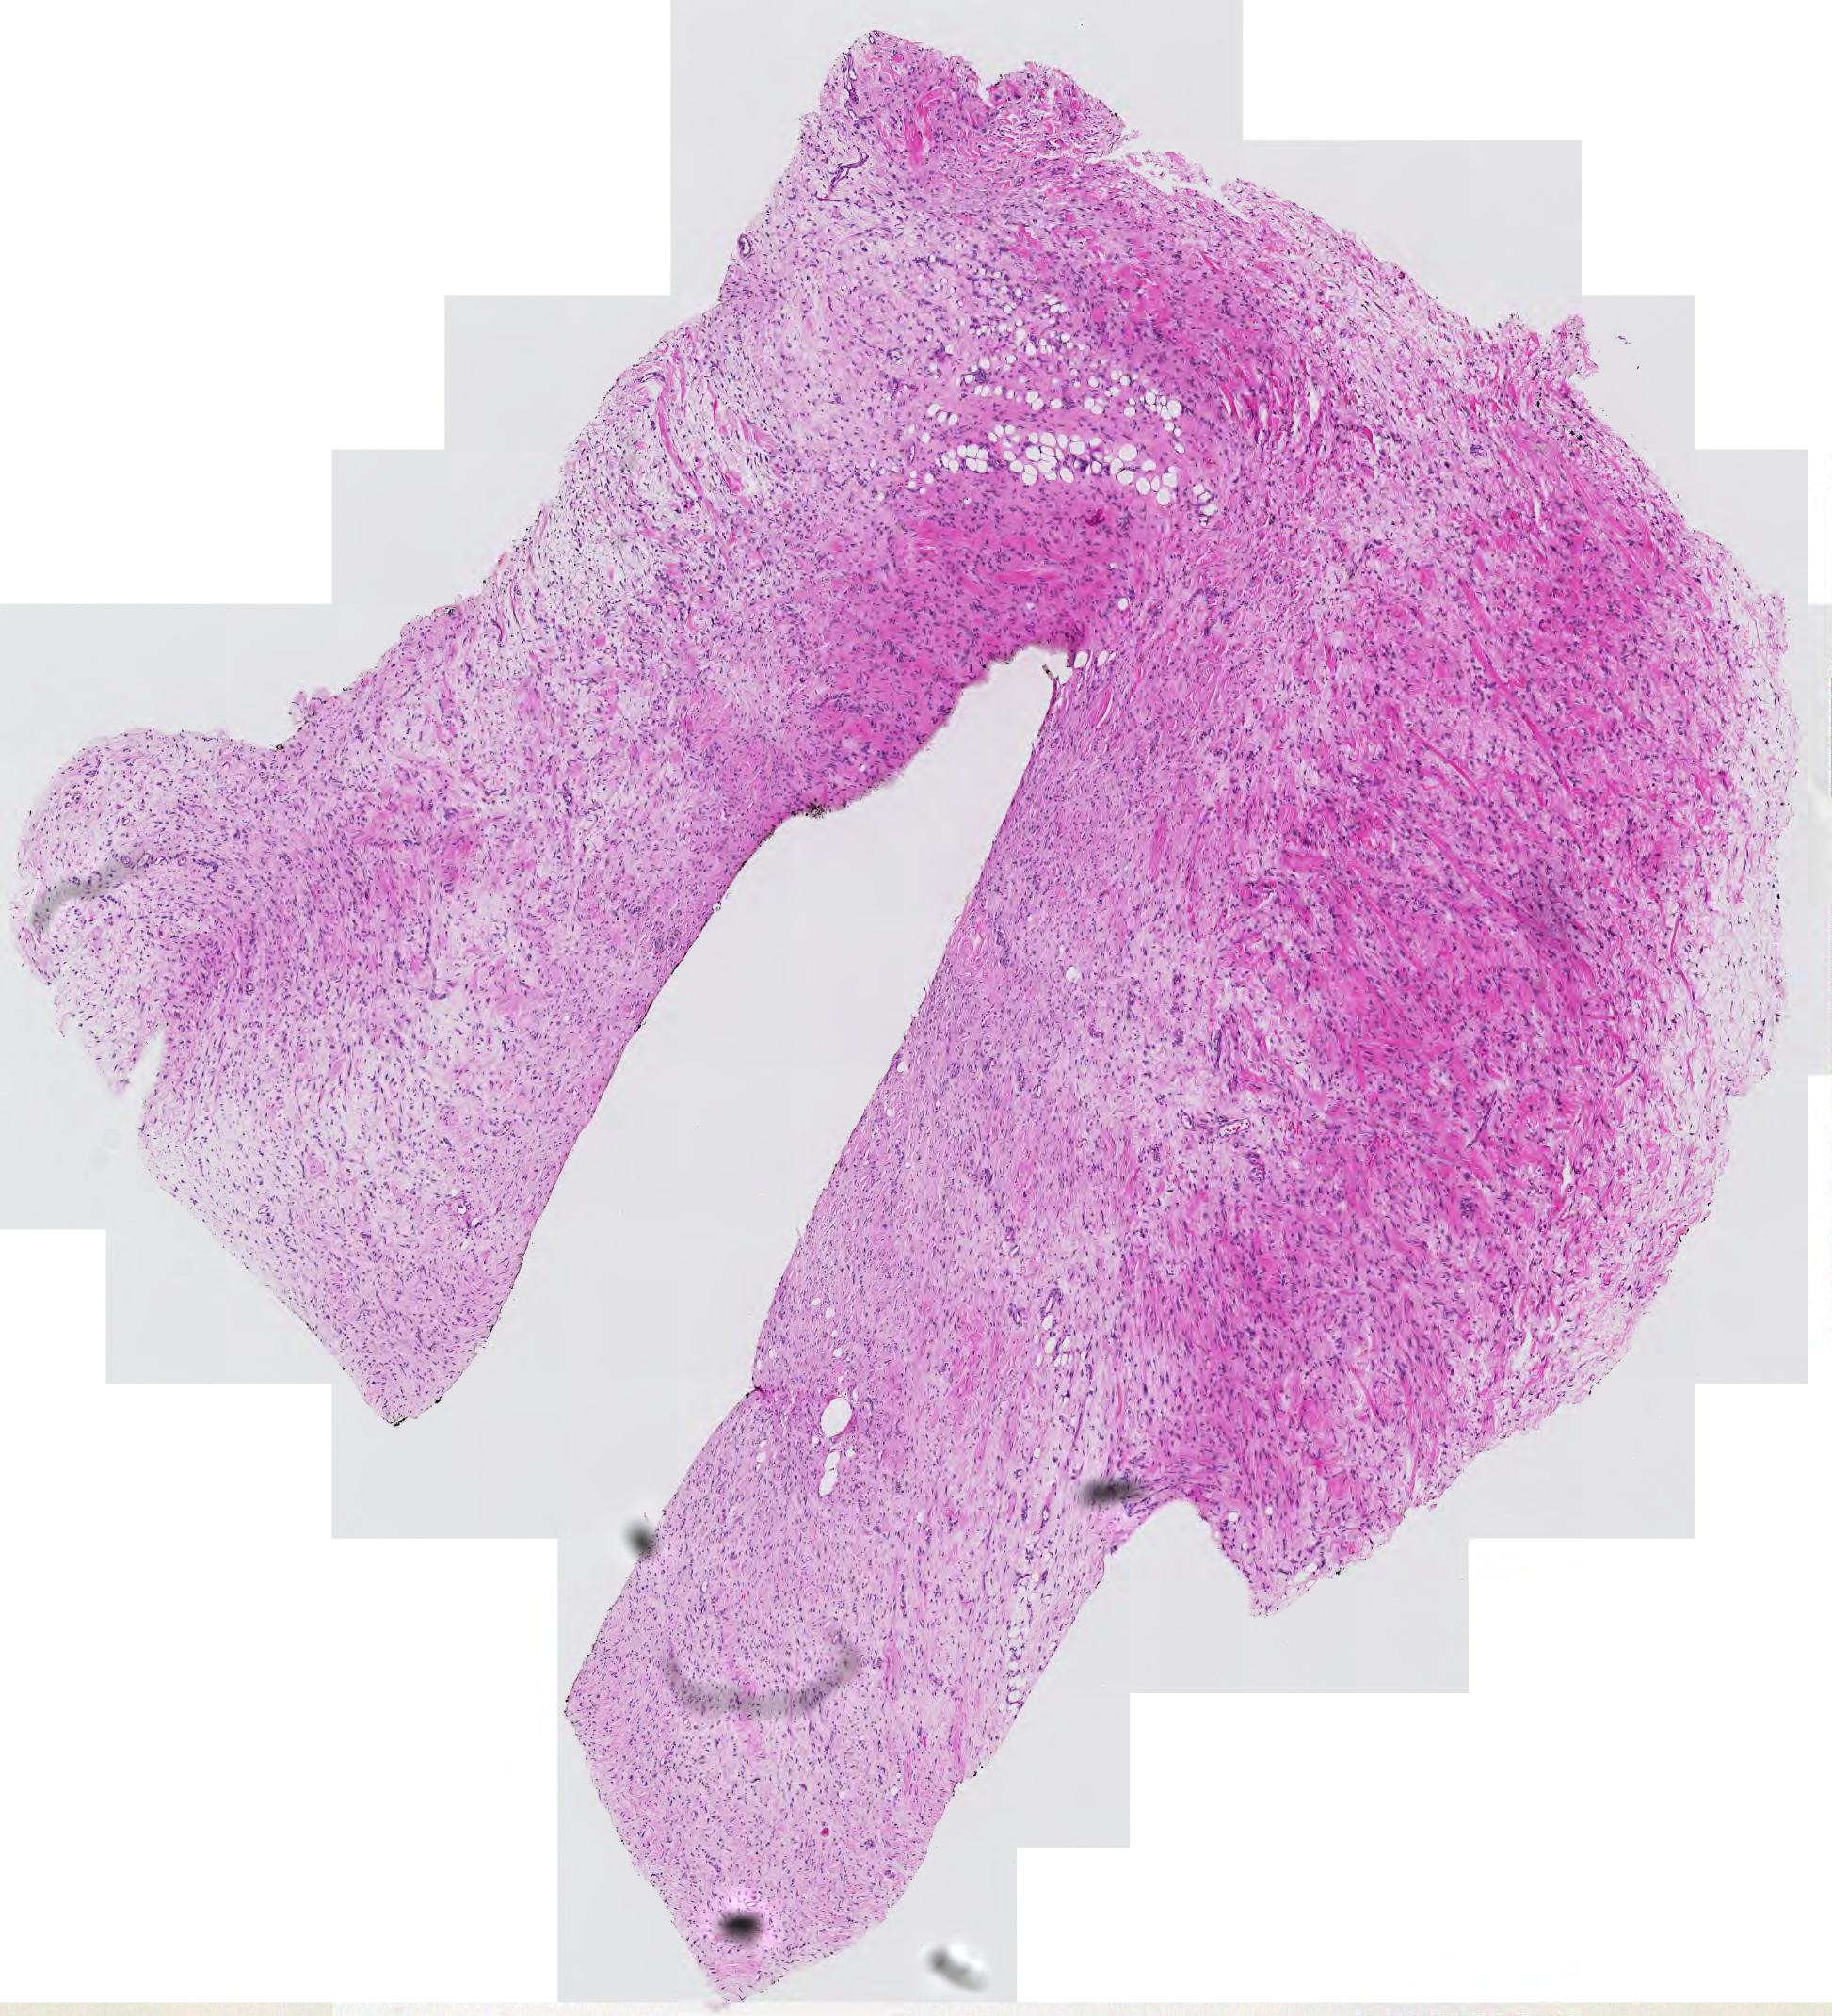
Digitized H&E-stained tissue section (whole slide), low-resolution overview of the scanned area, about 5.0 x 5.5 mm. Tumour tissue sample. 72-year-old female patient.
Patient diagnosis (cohort enrolment): sarcoma (site not recorded at cohort level).